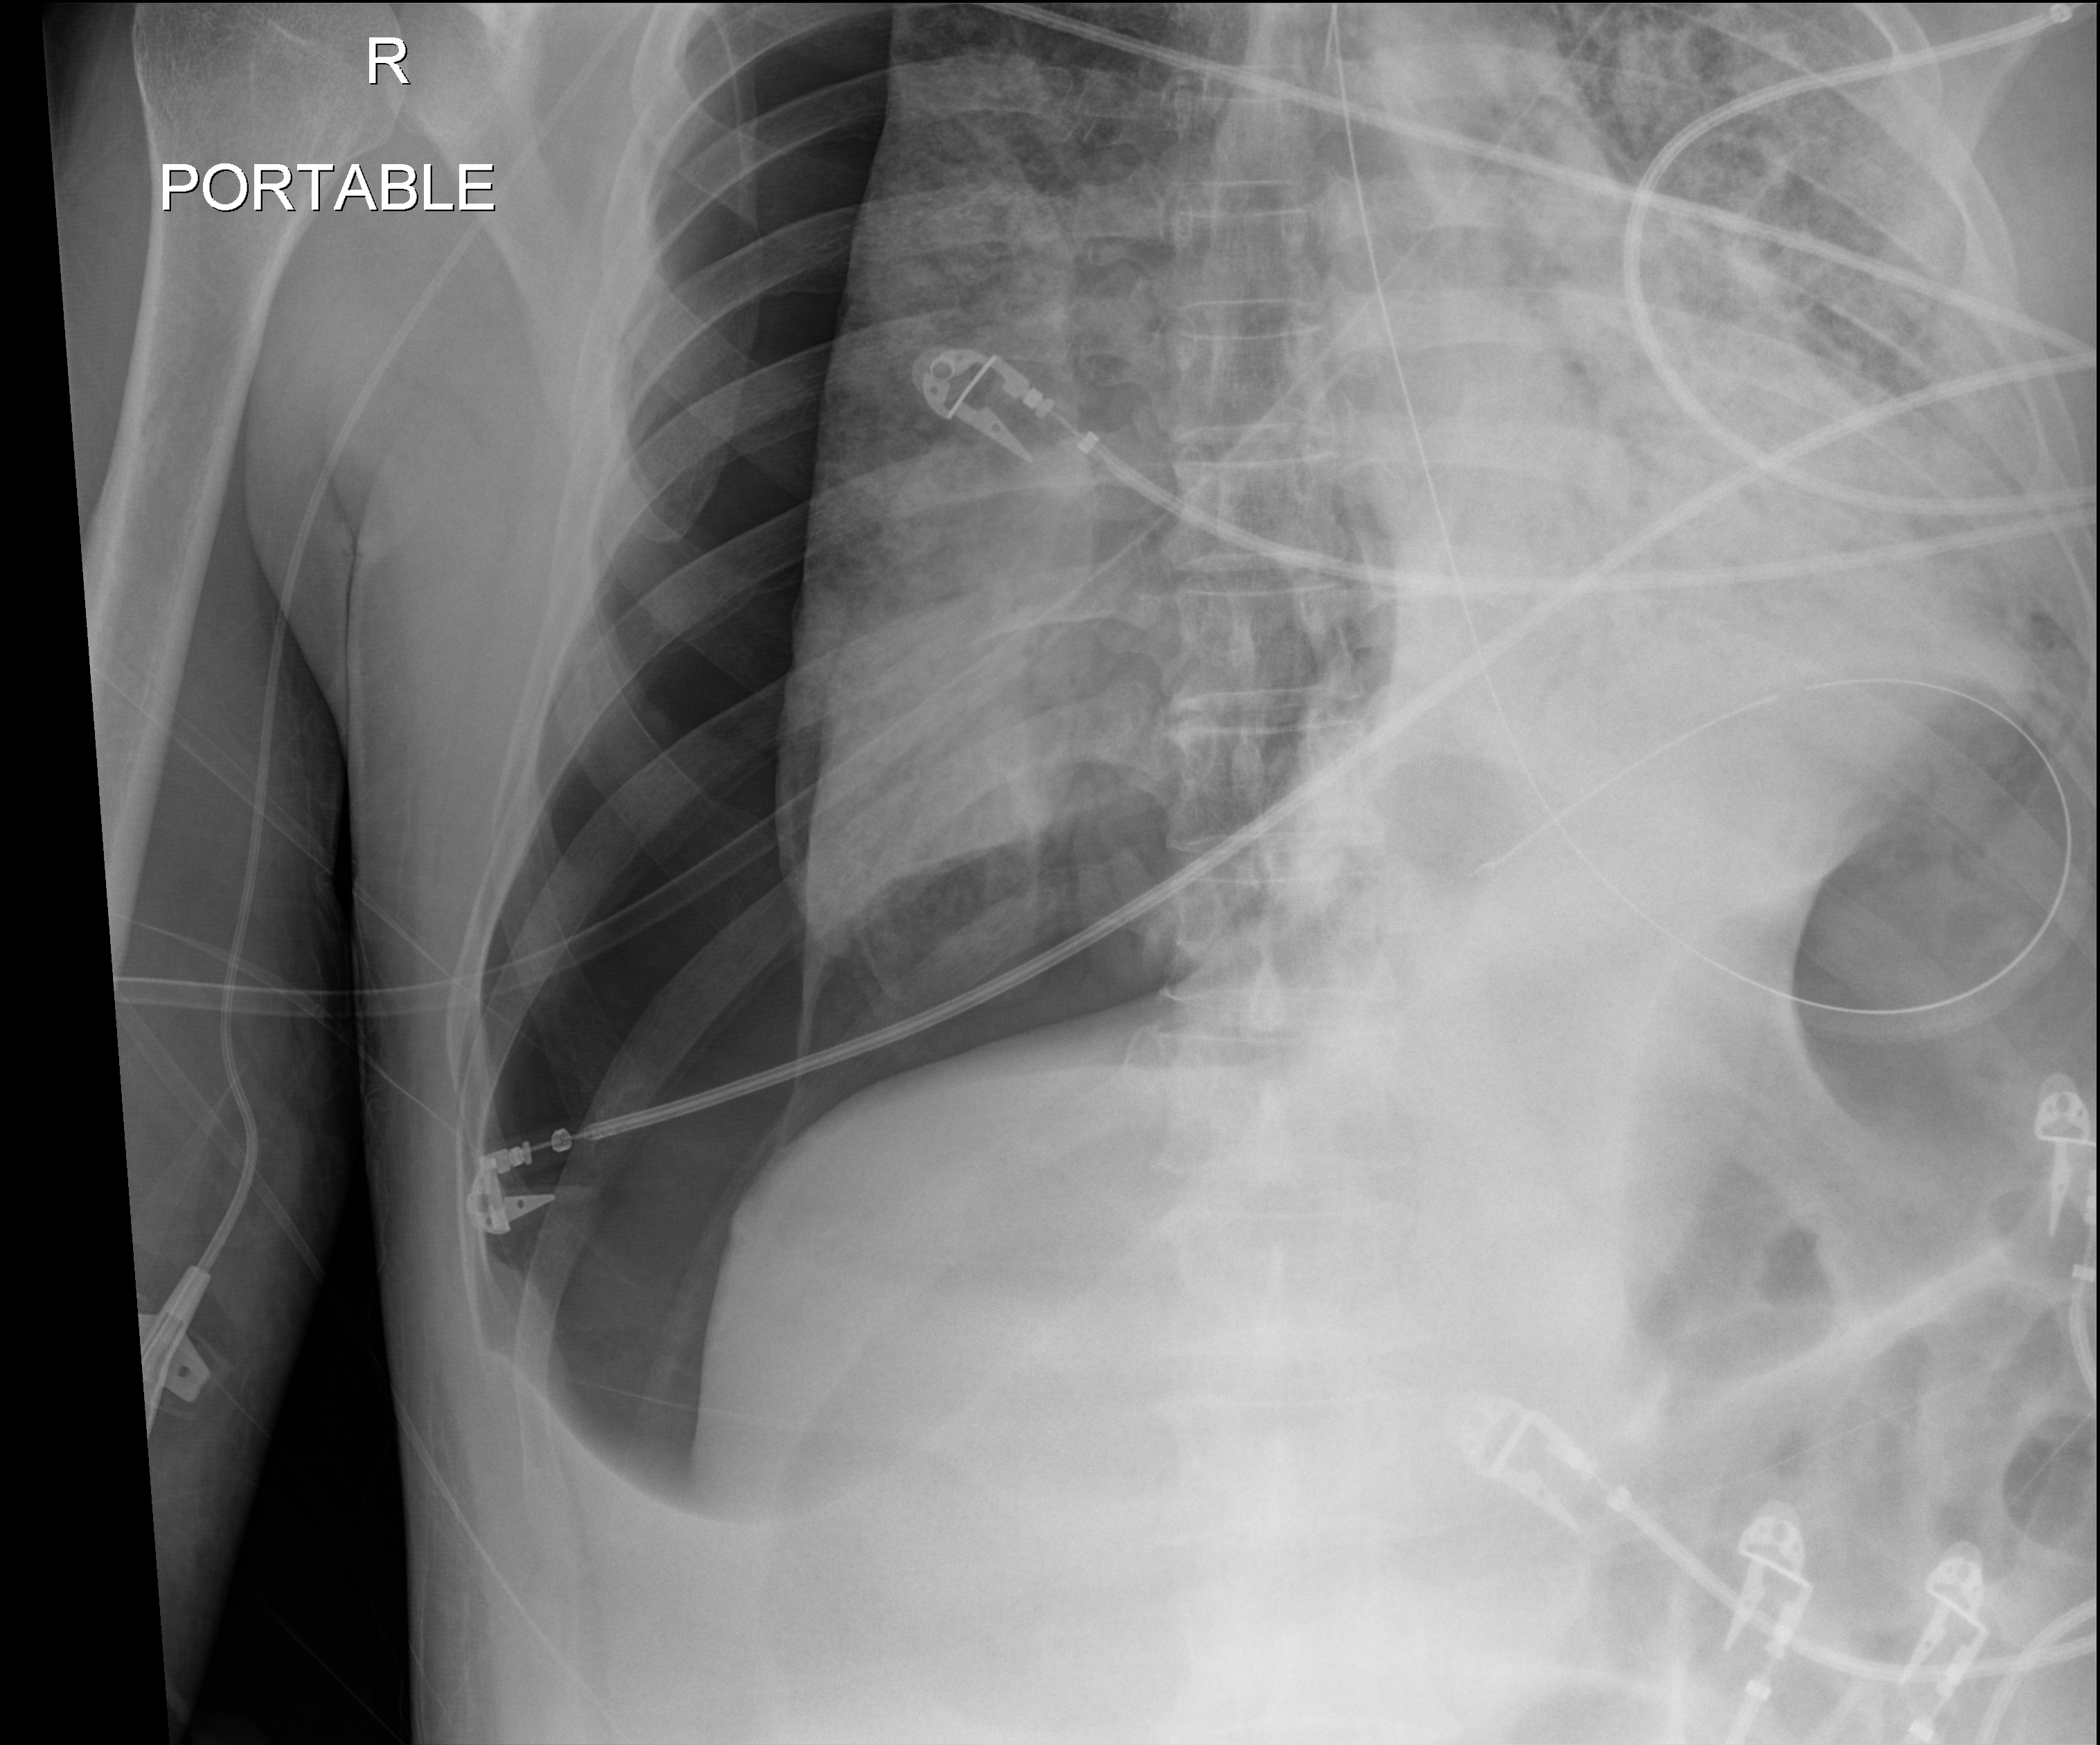
Chest radiograph, anteroposterior (AP) projection. Patient hospitalised with COVID-19; male, aged 60–74 years.
Admission-level facts for this patient (not findings on this image; timing relative to this image not recorded): hypertension (admission record): yes.